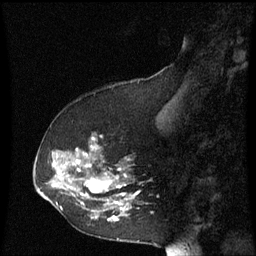
Breast MRI (dynamic contrast-enhanced), one sagittal slice; position 23 of 60 along the scan axis; dynamic contrast-enhanced series, image 2 of 3 at this slice position (ordered by acquisition); 1.5 T; TE 4.2 ms, TR 8.9 ms; 2 mm slice thickness; 256 × 256 image matrix, field of view 200 × 200 mm. Patient: female, 53 years. From the clinical record (not read from this slice): setting: breast cancer imaged before/during neoadjuvant chemotherapy; receptor status: HR-positive, HER2-negative.
Outlined on this slice (semi-automatically segmented with operator editing):
- analysis volume of interest (the breast-tissue region the enhancement analysis was run in; not a lesion): bounding box (x1, y1, x2, y2) in pixels: (38, 134, 141, 223)
- tumour enhancement mask (voxels above the 70 % enhancement threshold inside the analysis volume of interest): (58, 138, 139, 221)